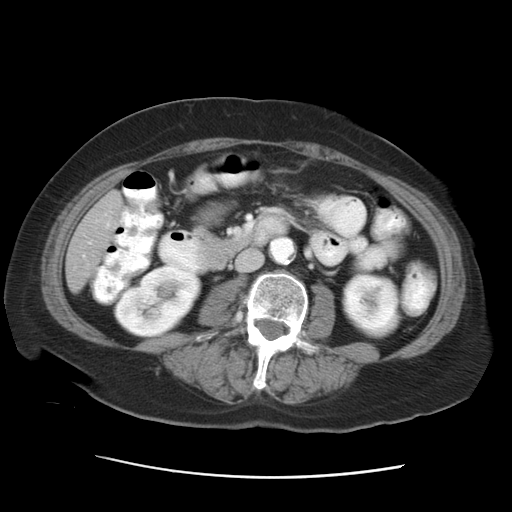
Contrast-enhanced abdominal CT, one axial slice. Position 8 of 29 along the scan axis. Reconstruction kernel STANDARD. 120 kVp. Intravenous contrast given. Soft-tissue window (W 400 / L 40 HU). 512 × 512 image matrix, field of view 354 × 354 mm. Female patient, age 64 years. From the clinical record (not read from this slice): diagnosis: colorectal cancer liver metastases, imaged before liver resection; multiple liver metastases: no; largest metastasis: 2.5 cm; disease in both lobes: no.
Structures marked on this image (expert manual segmentation):
- liver: bounding box <66,192,123,292> (left, top, right, bottom; pixels)
- planned liver remnant (the part of the liver to remain after resection): <66,191,124,292>